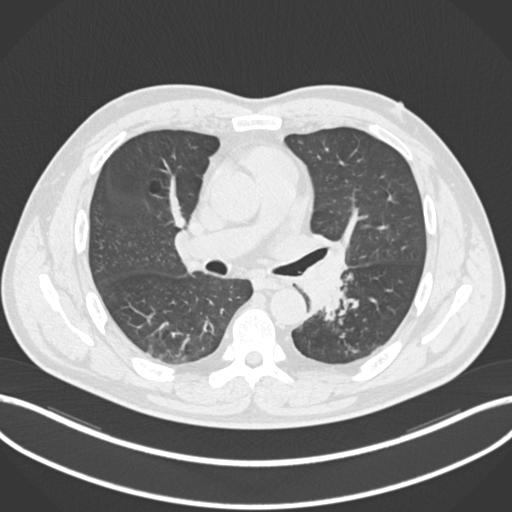
Chest CT, one axial slice; slice 129 of 223 in the series (ordered by position); reconstruction kernel B30f; lung window (W 1500 / L -600 HU); 512 × 512 image matrix, field of view 400 × 400 mm. Patient: male, 50 years. Case-level facts recorded for this patient, not image findings: clinical TNM (as recorded): T2a N3 M0.
Structures marked on this image (rectangle marked by the reading radiologist):
- lung tumour (recorded histology: squamous cell carcinoma): bounding box <295,244,352,322> (left, top, right, bottom; pixels)